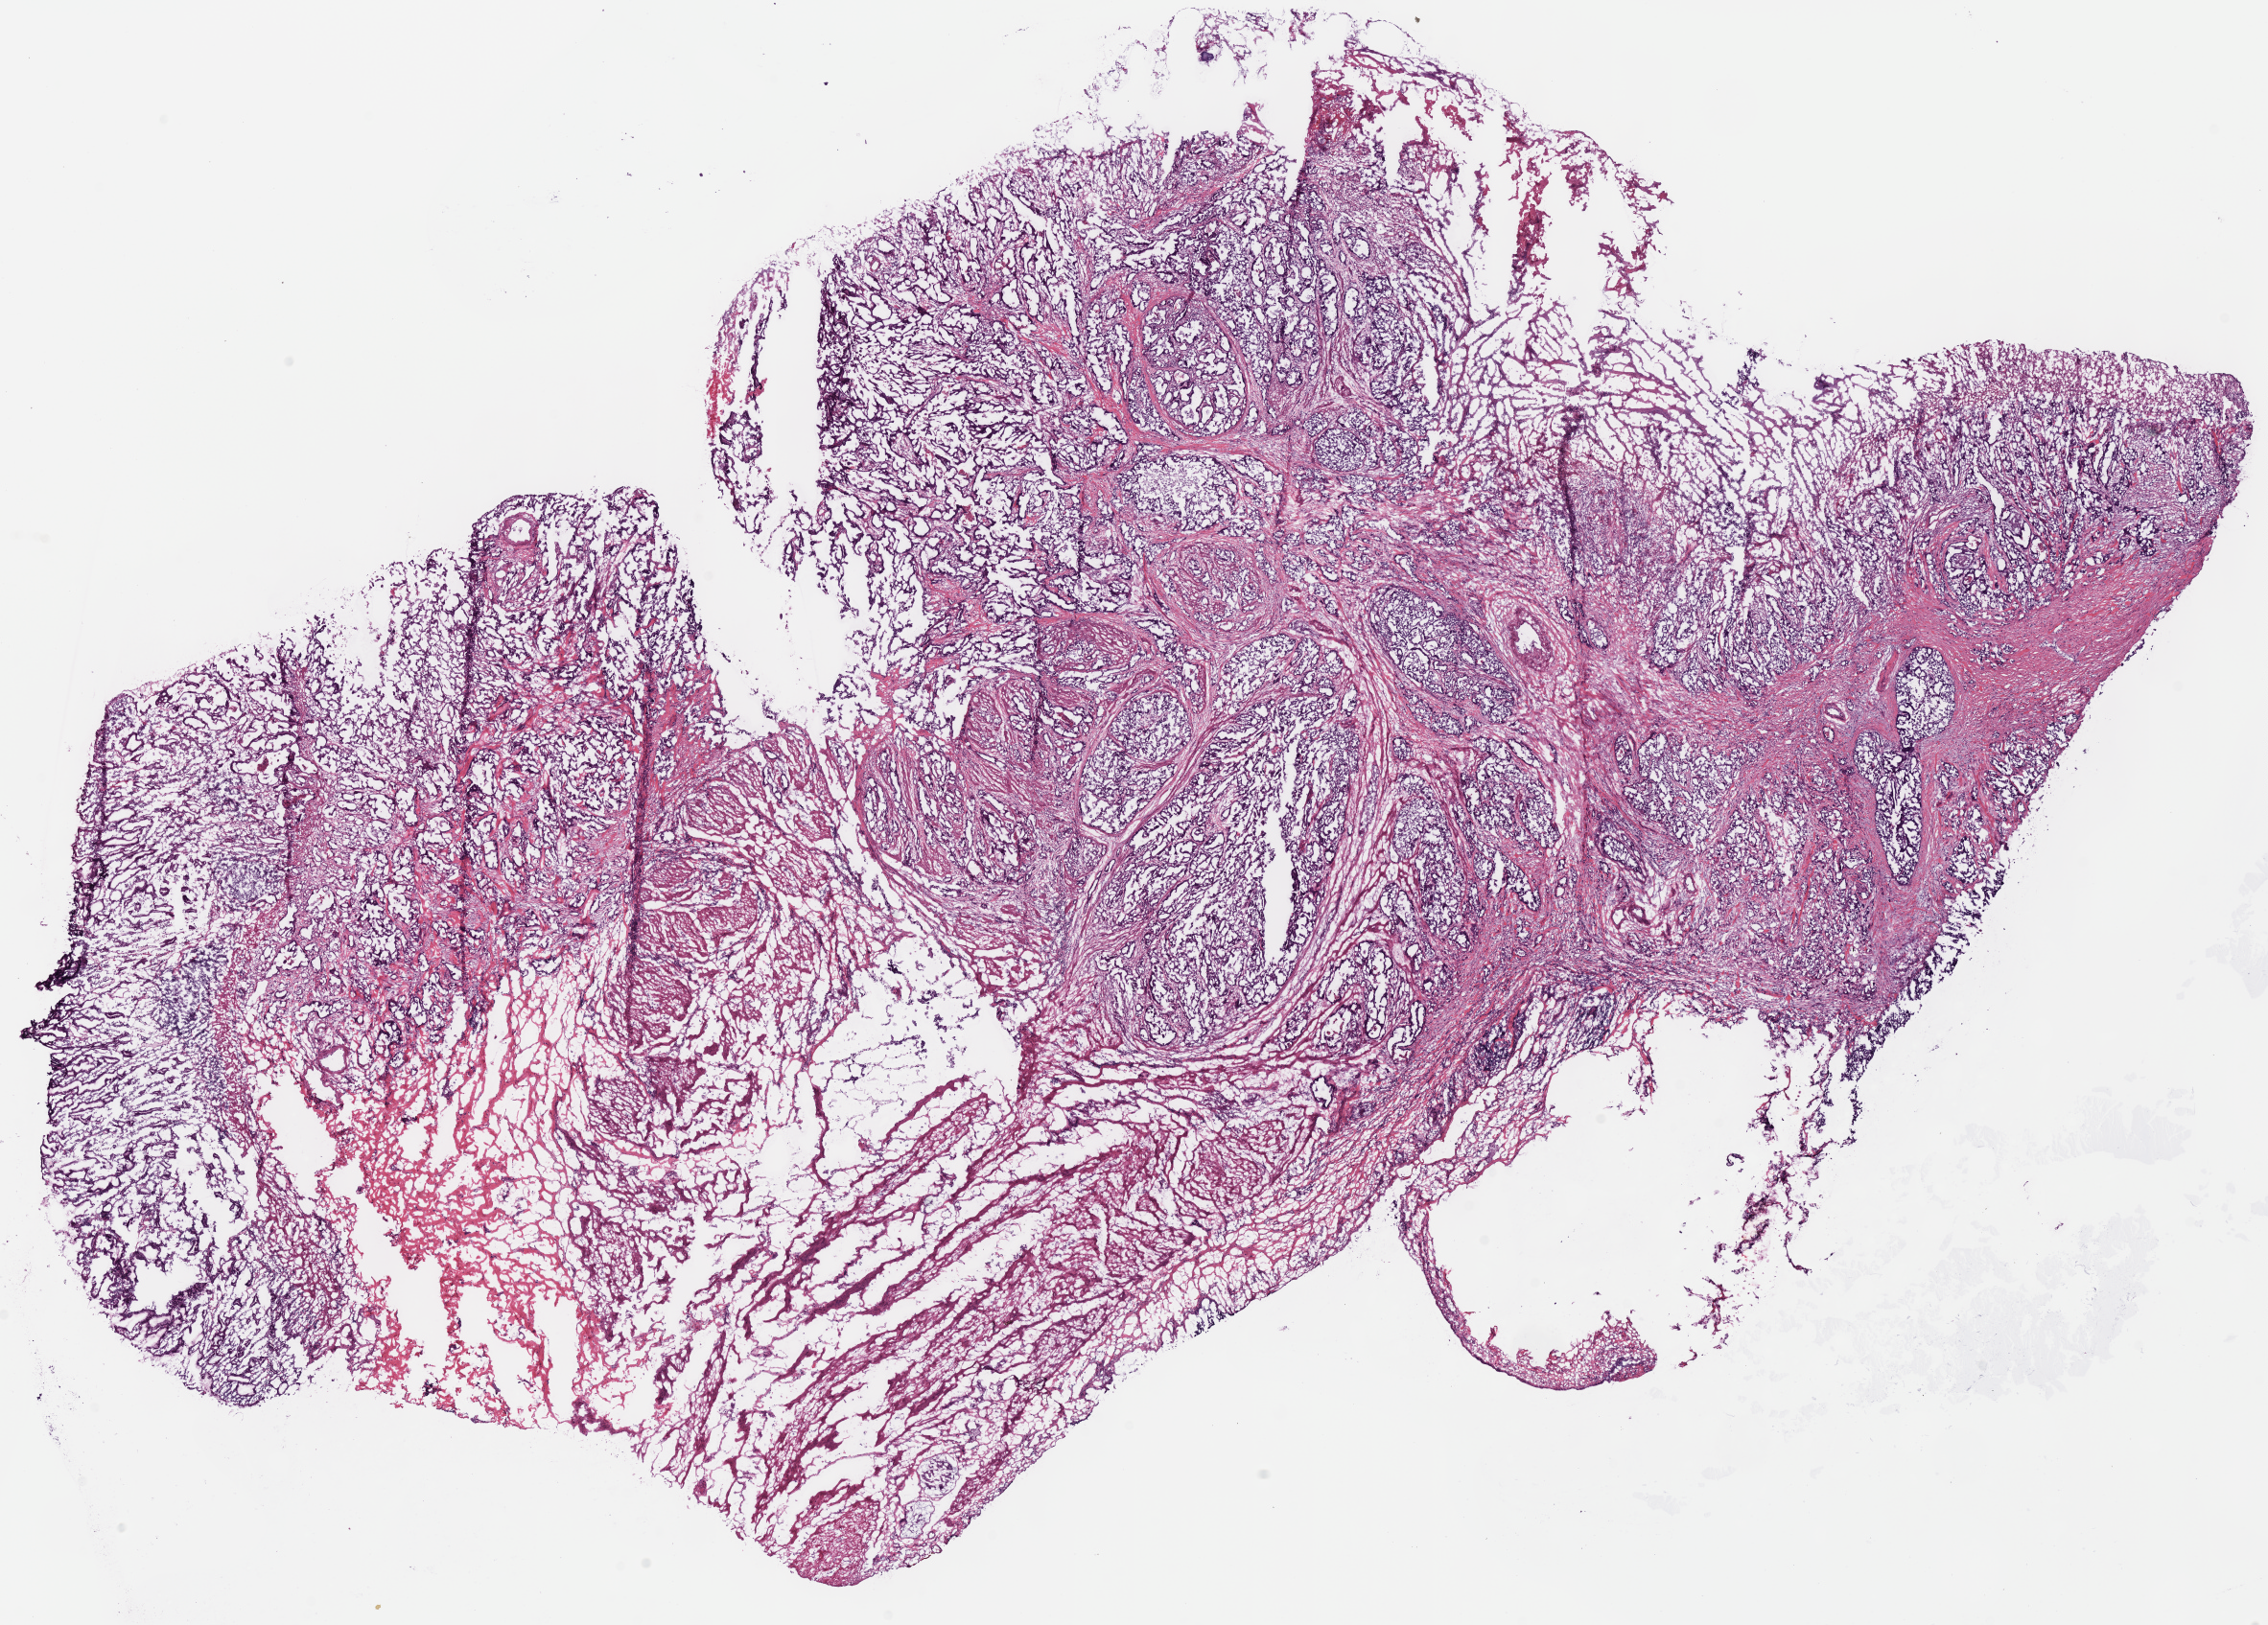
Hematoxylin and eosin (H&E) stained whole-slide image — whole scanned area (about 18.6 x 13.3 mm, from a 40x scan) shown as a low-resolution overview; frozen section from the bottom of the tissue portion; sample: primary tumour, stomach. Male patient; age at initial diagnosis 63 years. Histologic grade: G2 (moderately differentiated). Pathologist review of this section (percent, as recorded): tumour cells 80%, tumour nuclei 71%, normal cells 5%, stromal cells 14%, necrosis 1%. Infiltration values recorded for this section: lymphocyte infiltration 15%, monocyte infiltration 0%, neutrophil infiltration 0%.
* TNM: T4 N1 M0
* lymph nodes positive (case pathology): 2 of 6 examined
* AJCC pathologic stage: IV (6th edition)
* histologic diagnosis: Adenocarcinoma, NOS (cardia, NOS)